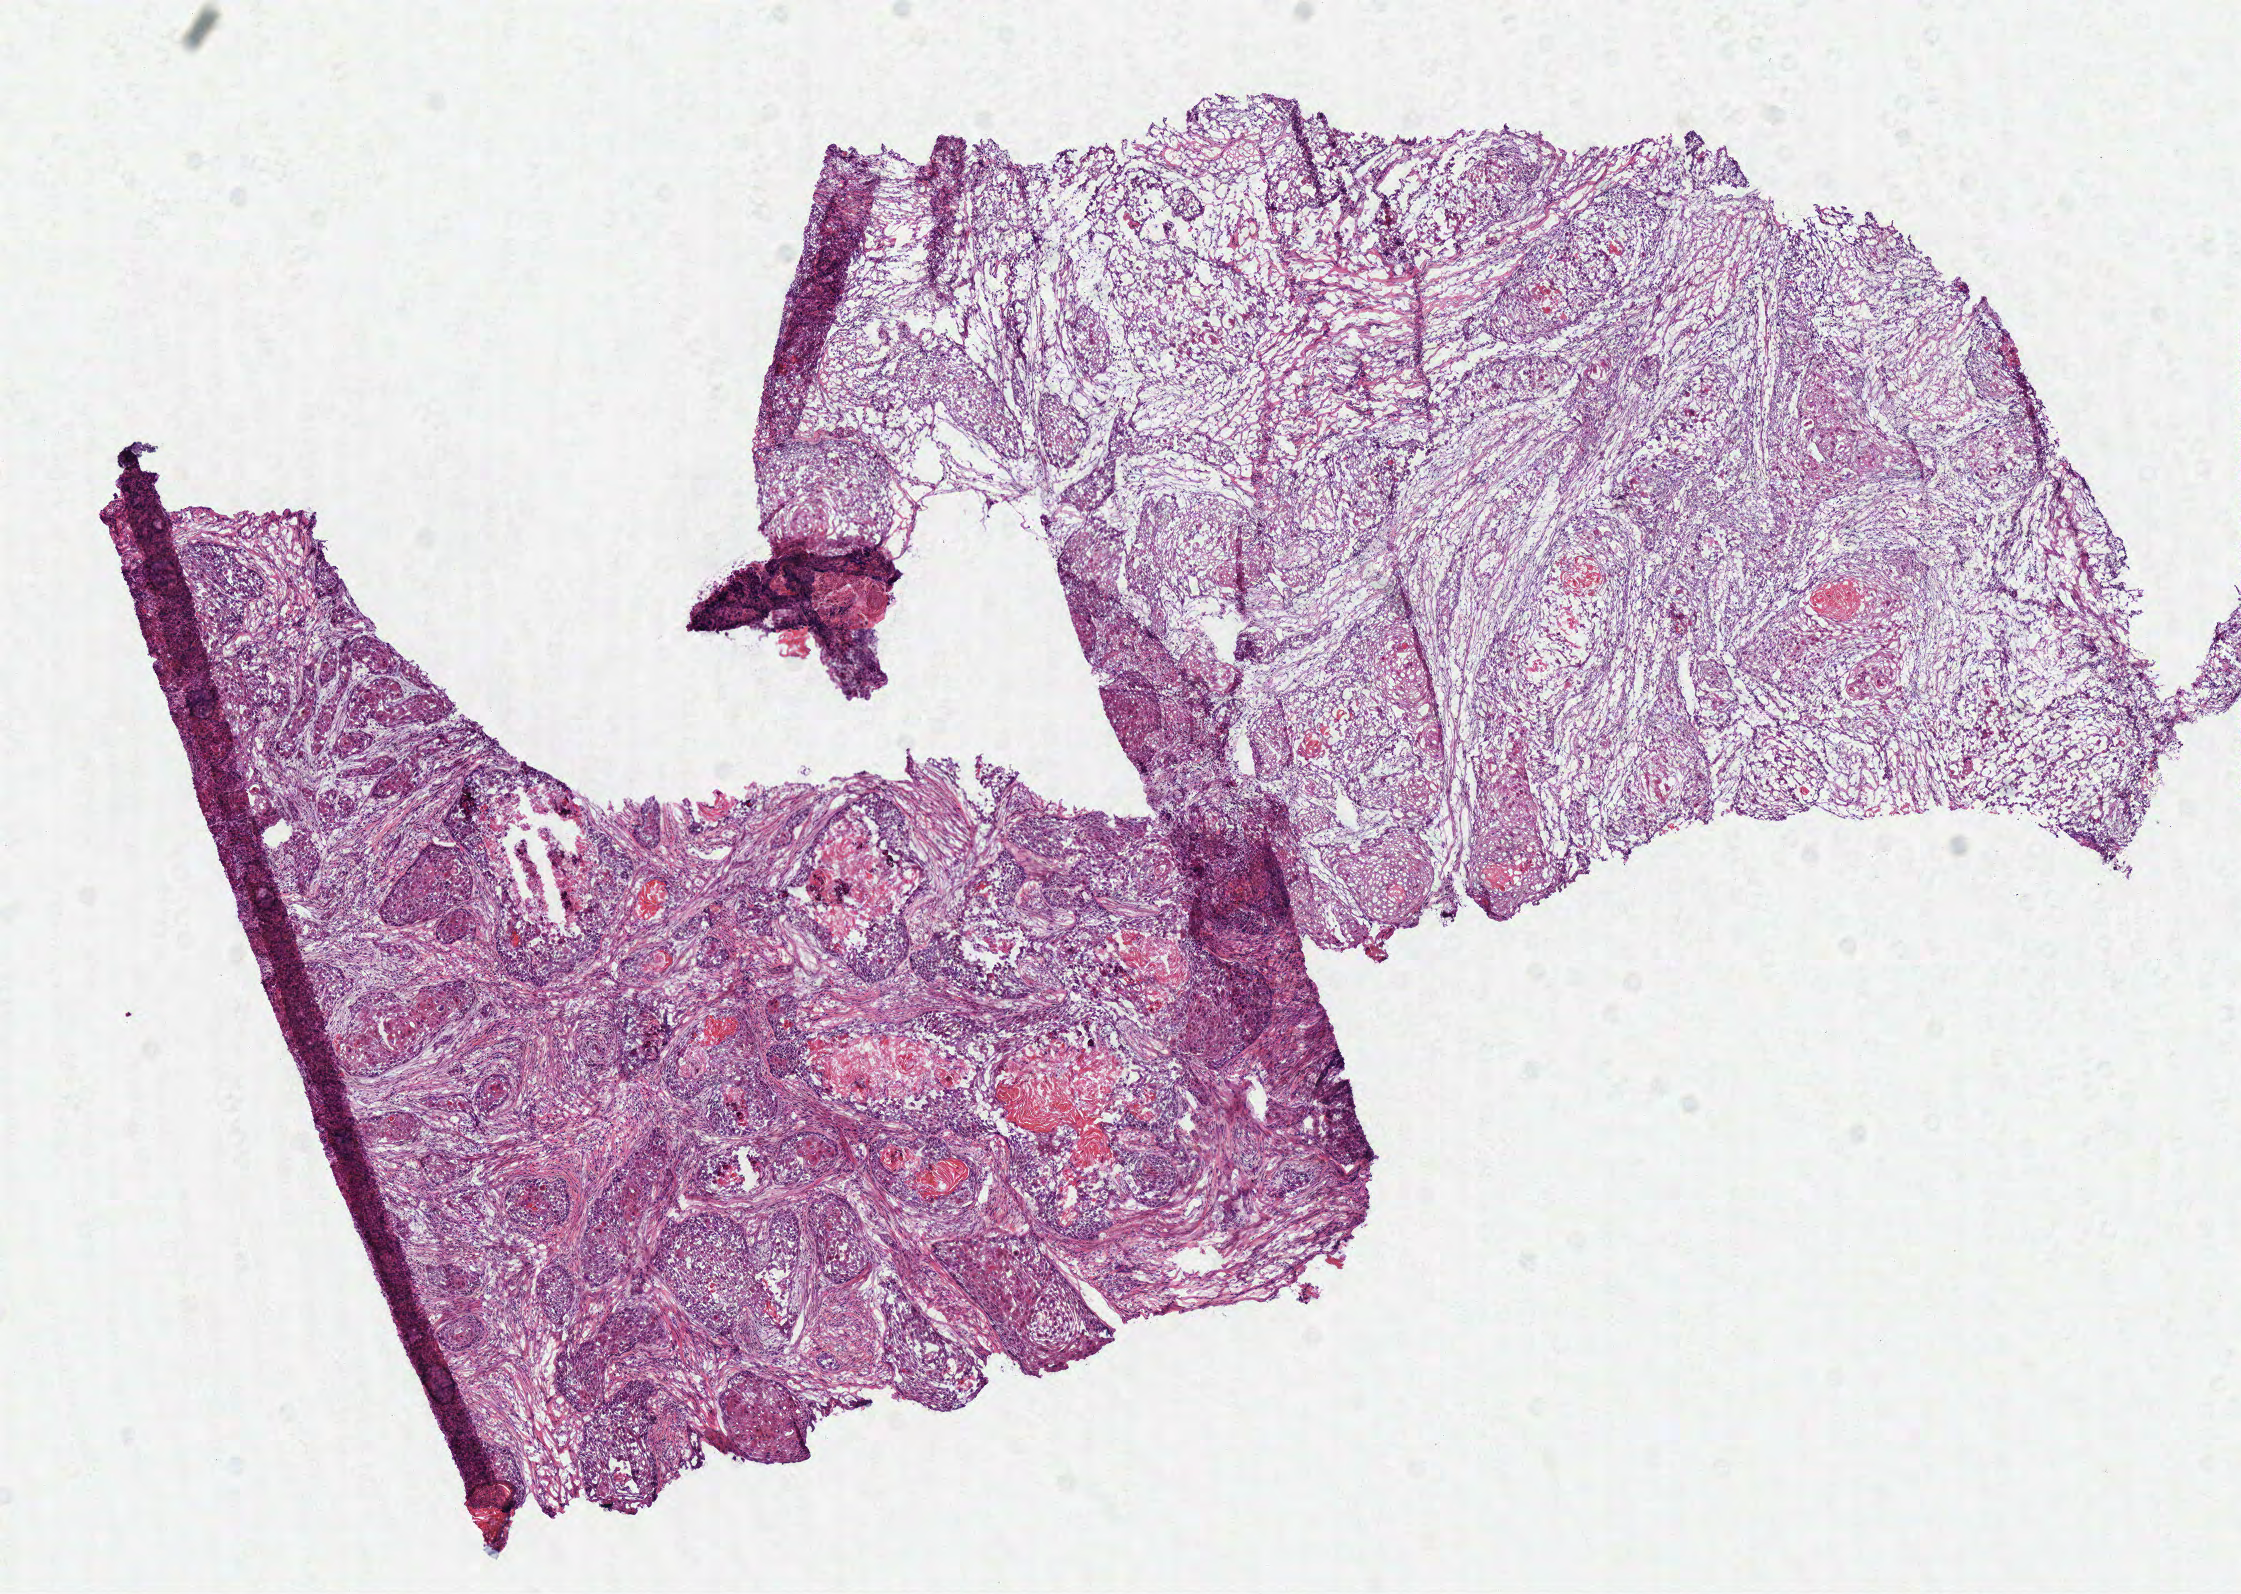
Whole-slide histology image, H&E, shown as a low-resolution overview of the whole scanned area (about 8.8 x 6.3 mm, acquisition: 40x scan). Frozen section. Primary tumour sample from the head and neck. Male patient; age at initial diagnosis 67 years. Histologic grade: G2 (moderately differentiated). Slide review estimates, as recorded: tumour cells 85%, tumour nuclei 75%, normal cells 0%, stromal cells 15%, necrosis 0%.
Lymph nodes positive (case pathology): 0 of 37 examined. Histologic diagnosis: Squamous cell carcinoma, NOS (overlapping lesion of lip, oral cavity and pharynx). AJCC pathologic stage: IVA (7th edition).